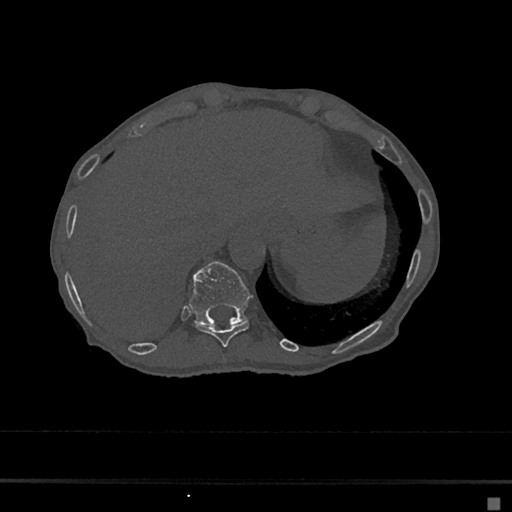
CT including the spine, one axial slice; slice 202 of 797 in the series (ordered by position); reconstruction kernel Br40s/3; bone window (W 1800 / L 400 HU); 0.5 mm slice thickness; 512 × 512 image matrix. Patient: female, 68 years. From the clinical record (not read from this slice): primary cancer: renal.
Annotated regions visible in this slice (semi-automatic segmentation, software-assisted and operator-edited):
- T10 vertebra: bounding box <195,320,249,347> (left, top, right, bottom; pixels)
- T11 vertebra: <189,262,252,325>